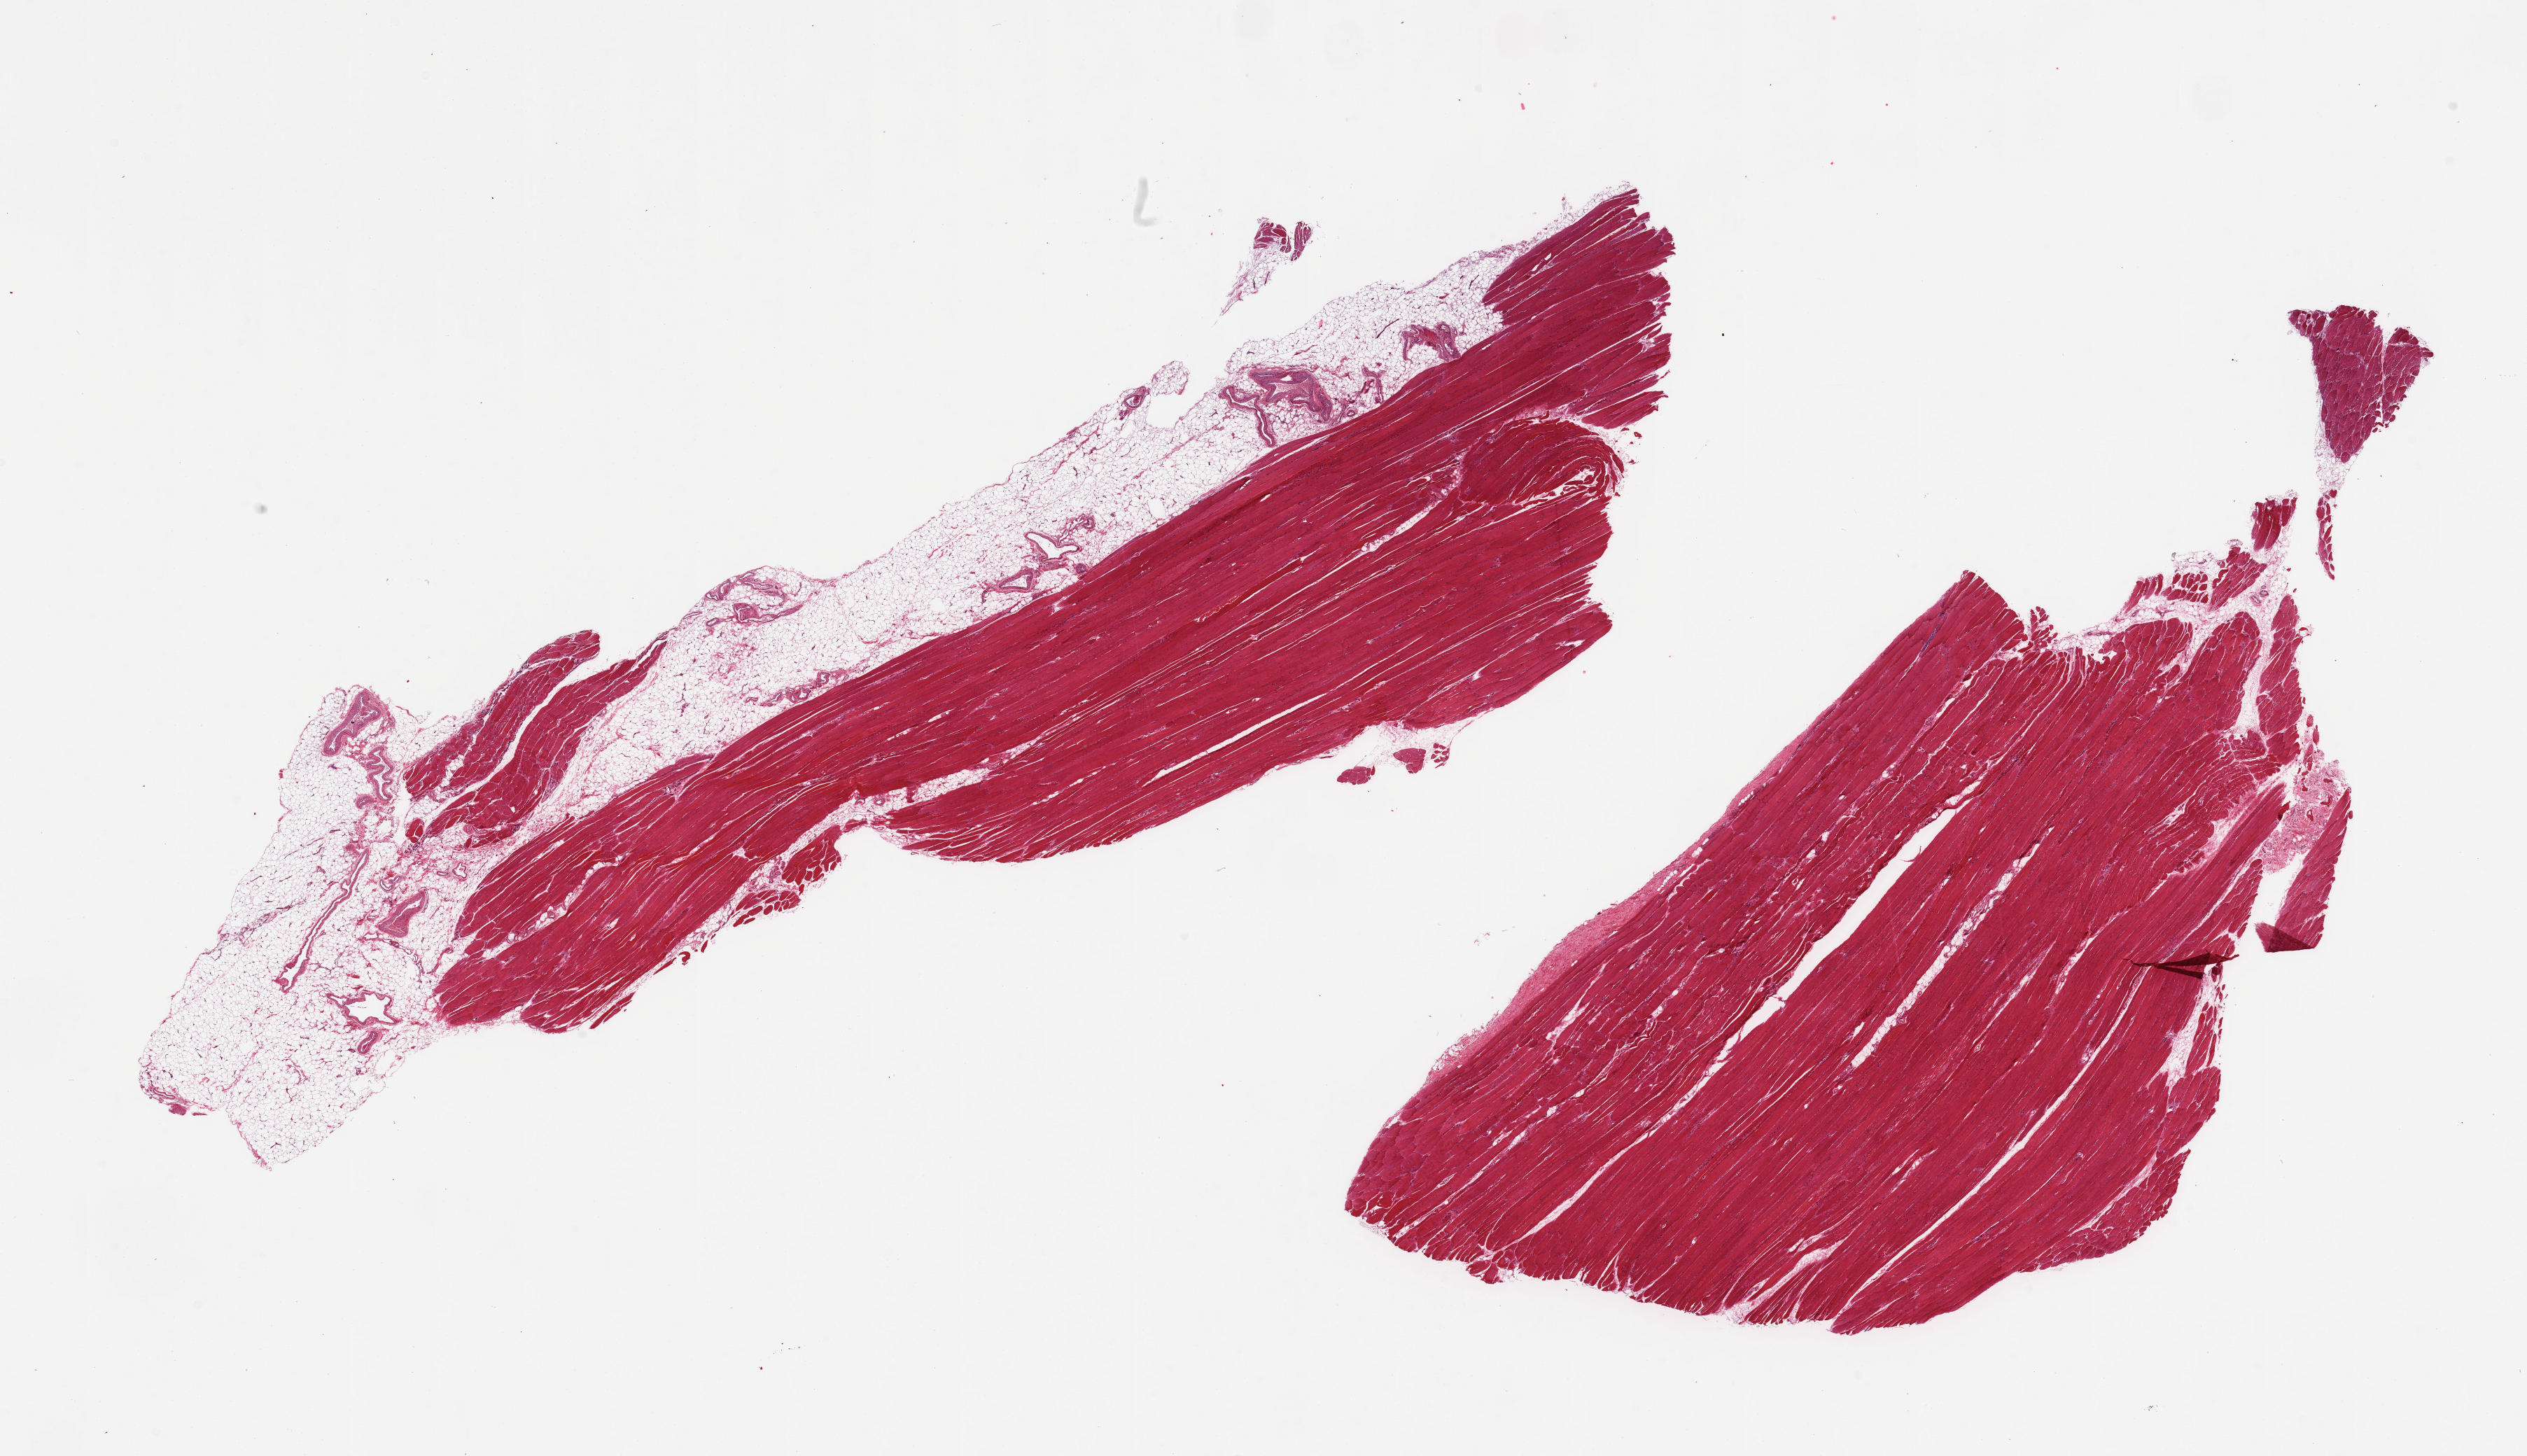
Digitized haematoxylin and eosin-stained section, brightfield, low-resolution overview of the scanned area, about 28.5 x 16.4 mm (acquisition: 20x scan), PAXgene-fixed paraffin-embedded (PFPE) section, sampled site (target tissue): skeletal muscle, tissue donor sample. Donor sex: male.
Pathologist's review note for this sample: 2 pieces, ~25% adherent/interstitial fat.